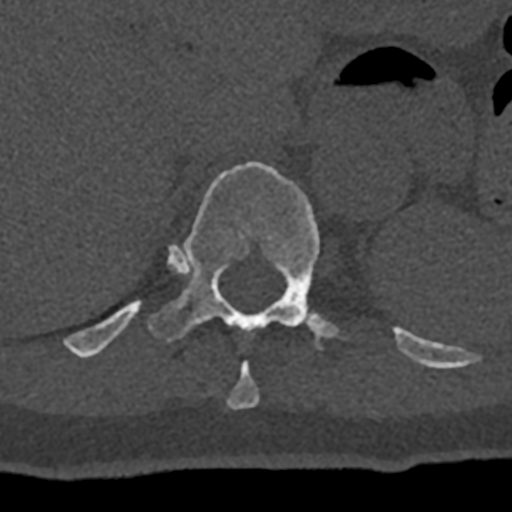
CT including the spine, one axial slice; position 552 of 797 along the scan axis; 120 kVp; bone window (W 1800 / L 400 HU); 0.5 mm slice thickness; 512 × 512 image matrix, field of view 160 × 160 mm. Male patient, age 74 years. Case-level facts recorded for this patient, not image findings: primary cancer: renal; vertebrae with lytic lesions (as recorded): T10, L1, L2, L3, L4, L5.
Annotated regions visible in this slice (semi-automatically segmented with operator editing):
- T10 vertebra: bounding box <227,361,260,409> (left, top, right, bottom; pixels)
- T11 vertebra: <70,162,432,367>